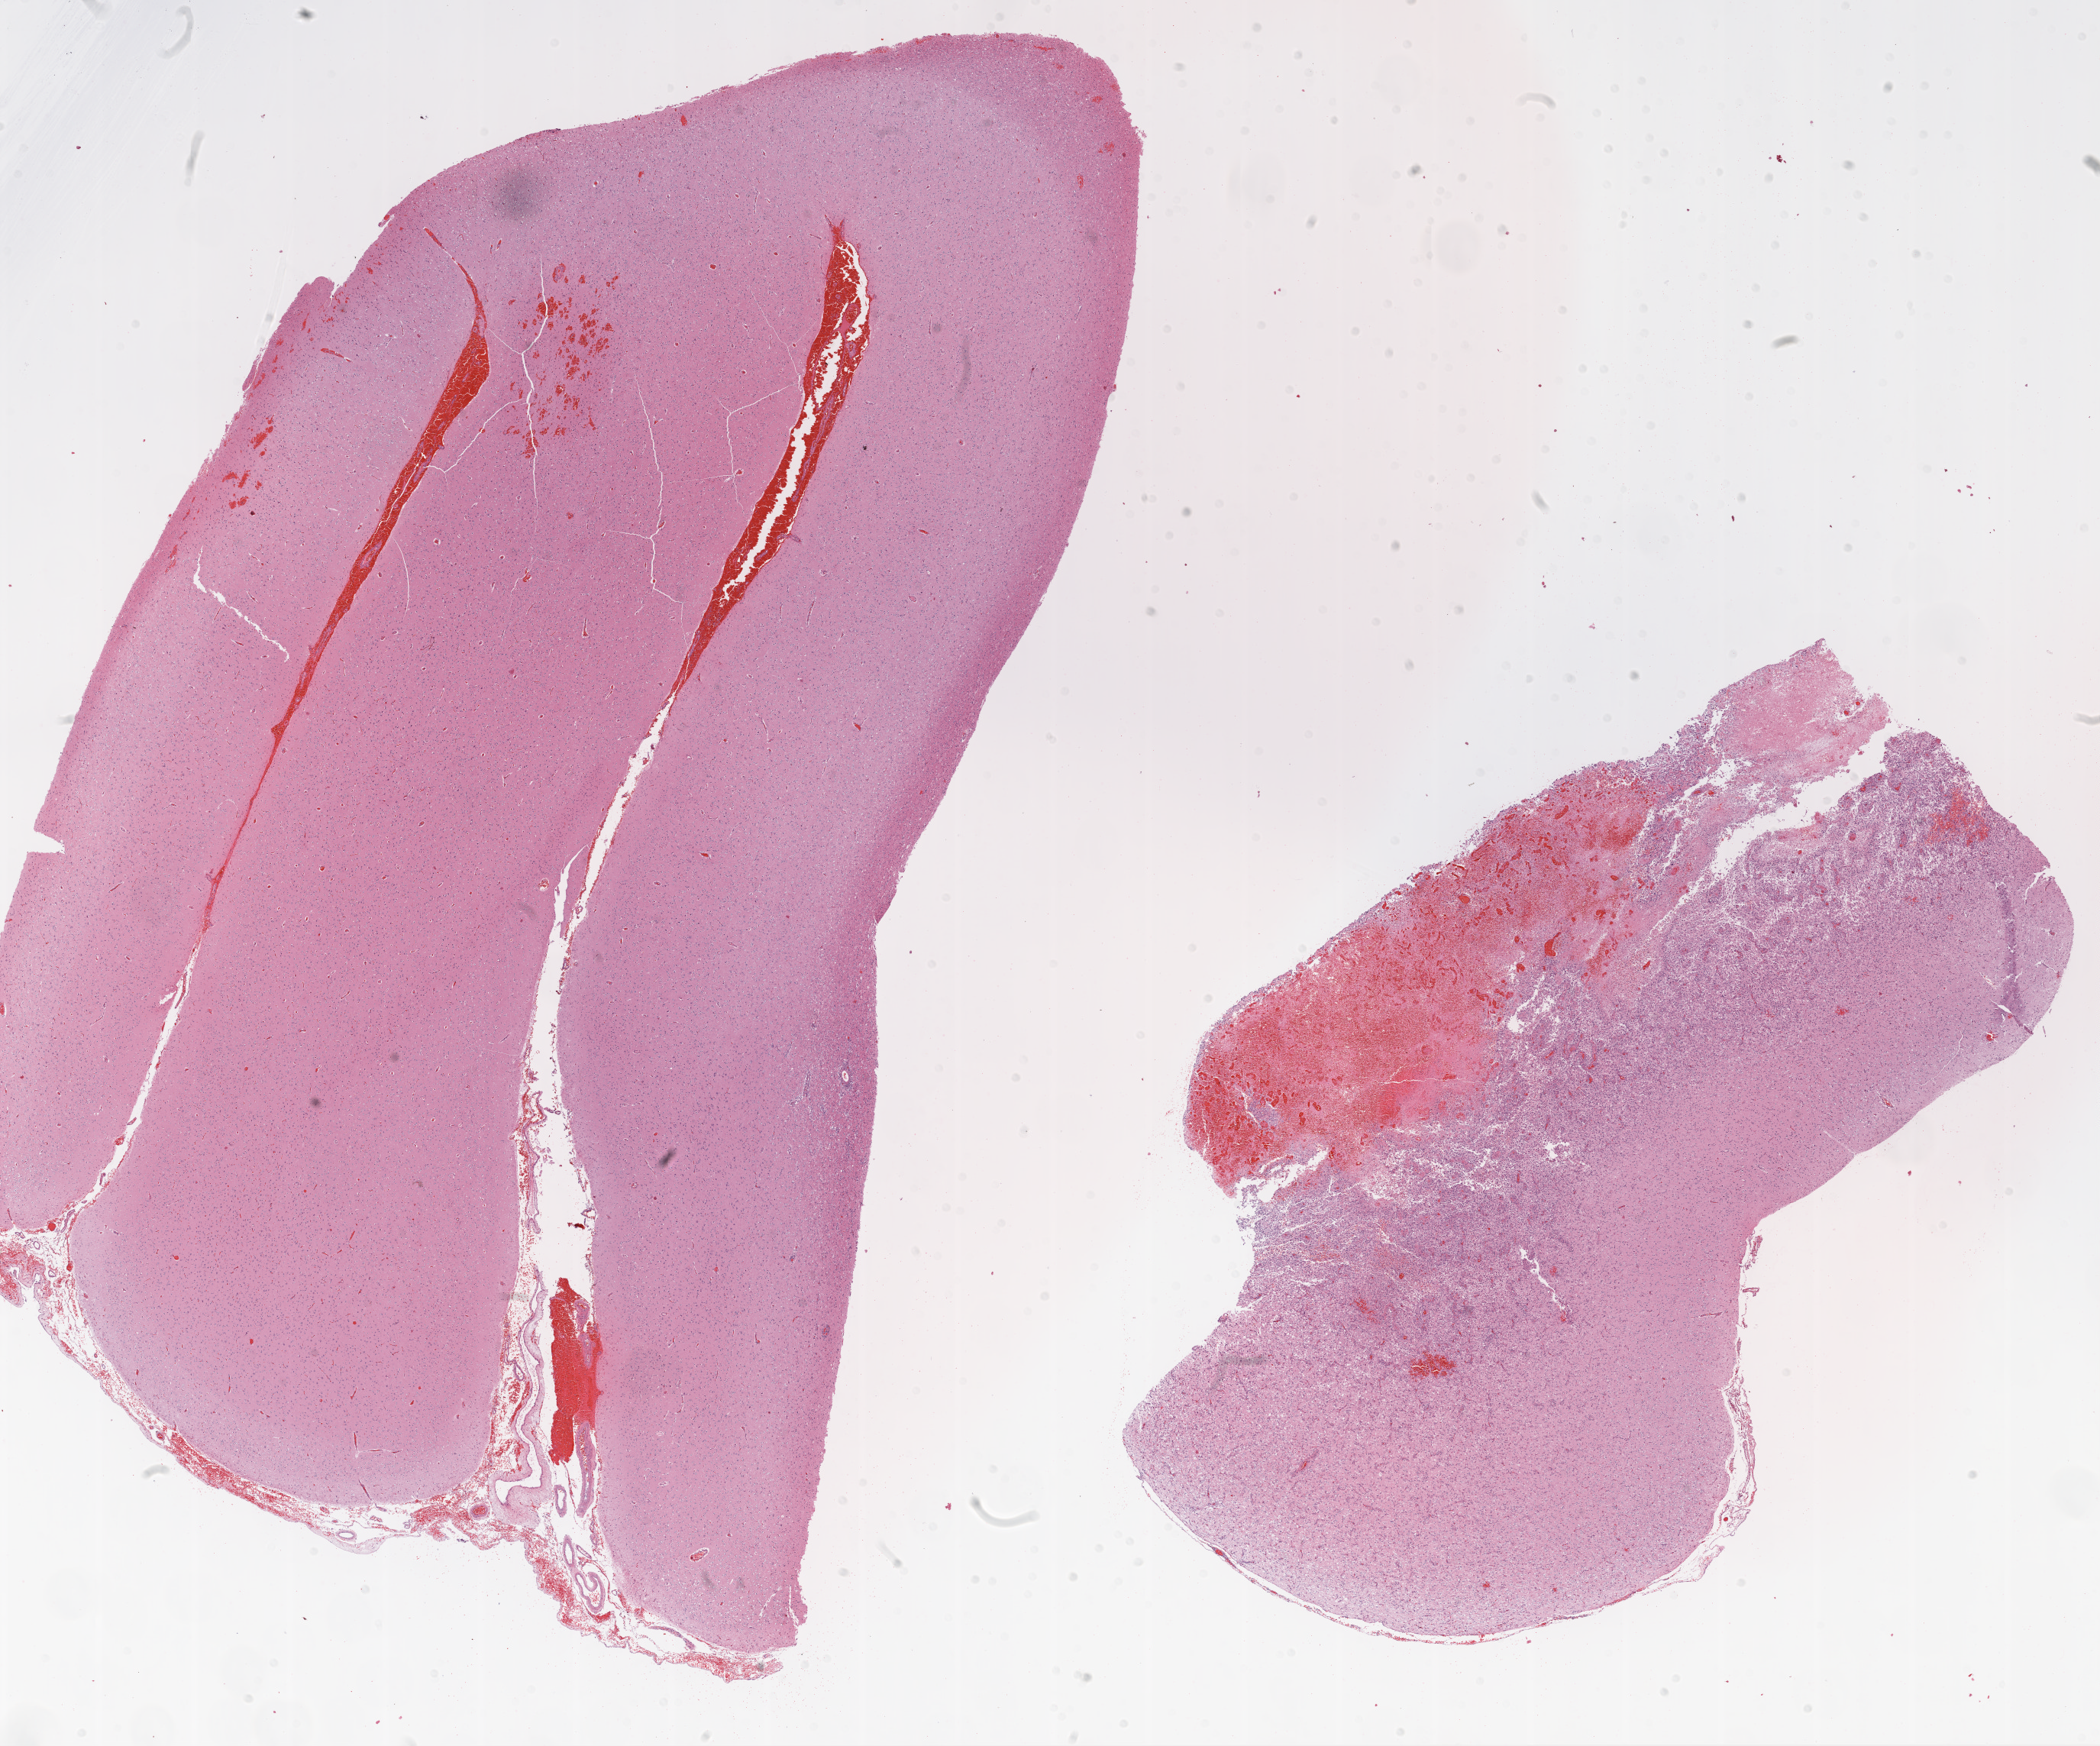
Hematoxylin and eosin (H&E) stained whole-slide image — shown as a low-resolution overview of the whole scanned area (about 22.1 x 18.3 mm, from a 20x scan); formalin-fixed paraffin-embedded (FFPE) diagnostic section; brain, primary tumour sample. Male patient; age at initial diagnosis 63 years.
Pathologic diagnosis: Glioblastoma.